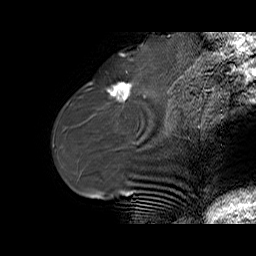
Breast MRI (dynamic contrast-enhanced), one sagittal slice; slice 22 of 70 in the series (ordered by position); dynamic contrast-enhanced series, time point 2 of 6 at this slice position (early post-contrast); 1.5 T; TE 5.5 ms, TR 32.9 ms; 4 mm slice thickness; 256 × 256 image matrix. Female patient. Case-level facts recorded for this patient, not image findings: setting: breast cancer imaged before/during neoadjuvant chemotherapy; receptor status: HER2-positive.
Outlined on this slice (semi-automatically segmented with operator editing):
- analysis volume of interest (the breast-tissue region the enhancement analysis was run in; not a lesion): box from (x=97, y=73) to (x=141, y=110) px
- tumour enhancement mask (voxels above the 100 % enhancement threshold inside the analysis volume of interest): (x=108, y=82)–(x=132, y=100)